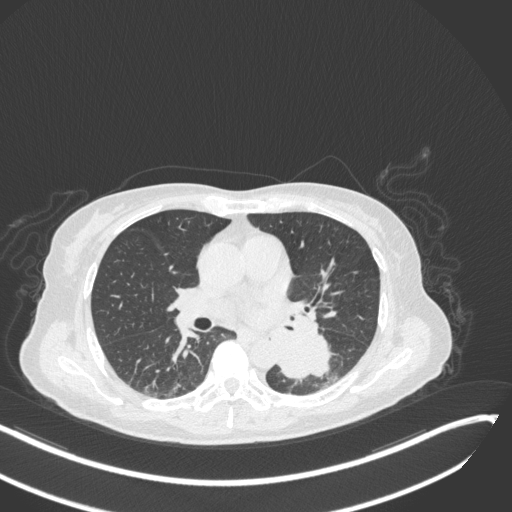
Chest CT, one axial slice. Position 147 of 342 along the scan axis. 120 kVp. Lung window (W 1500 / L -600 HU). 512 × 512 image matrix, field of view 400 × 400 mm. Female patient, age 64 years. From the clinical record (not read from this slice): clinical TNM (as recorded): T3 N1 M1; histopathological grade: G3.
Outlined on this slice (rectangle marked by the reading radiologist):
- lung tumour (recorded histology: small cell carcinoma): bounding box <273,322,337,382> (left, top, right, bottom; pixels)